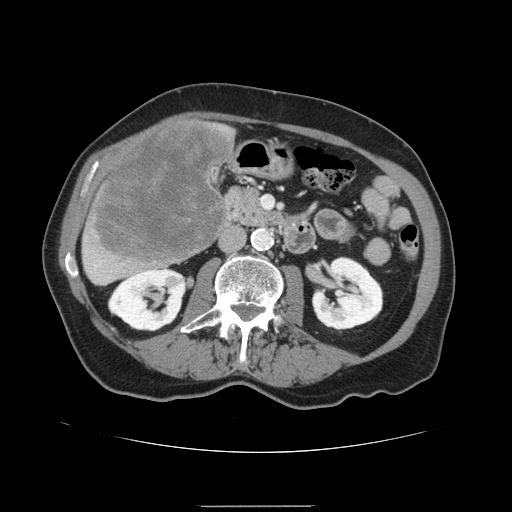
Contrast-enhanced abdominal CT, one axial slice. Slice 50 of 168 in the series (ordered by position). 120 kVp. Intravenous contrast given. Soft-tissue window (W 400 / L 40 HU). 2.5 mm slice thickness. 512 × 512 image matrix, field of view 386 × 386 mm. Male patient, age 74 years. Case-level facts recorded for this patient, not image findings: diagnosis: colorectal cancer liver metastases, imaged before liver resection; multiple liver metastases: no; largest metastasis: 14.5 cm.
Structures marked on this image (expert manual segmentation):
- liver: bounding box [x1, y1, x2, y2] px = [81, 118, 236, 286]
- liver metastasis: [93, 123, 235, 269]